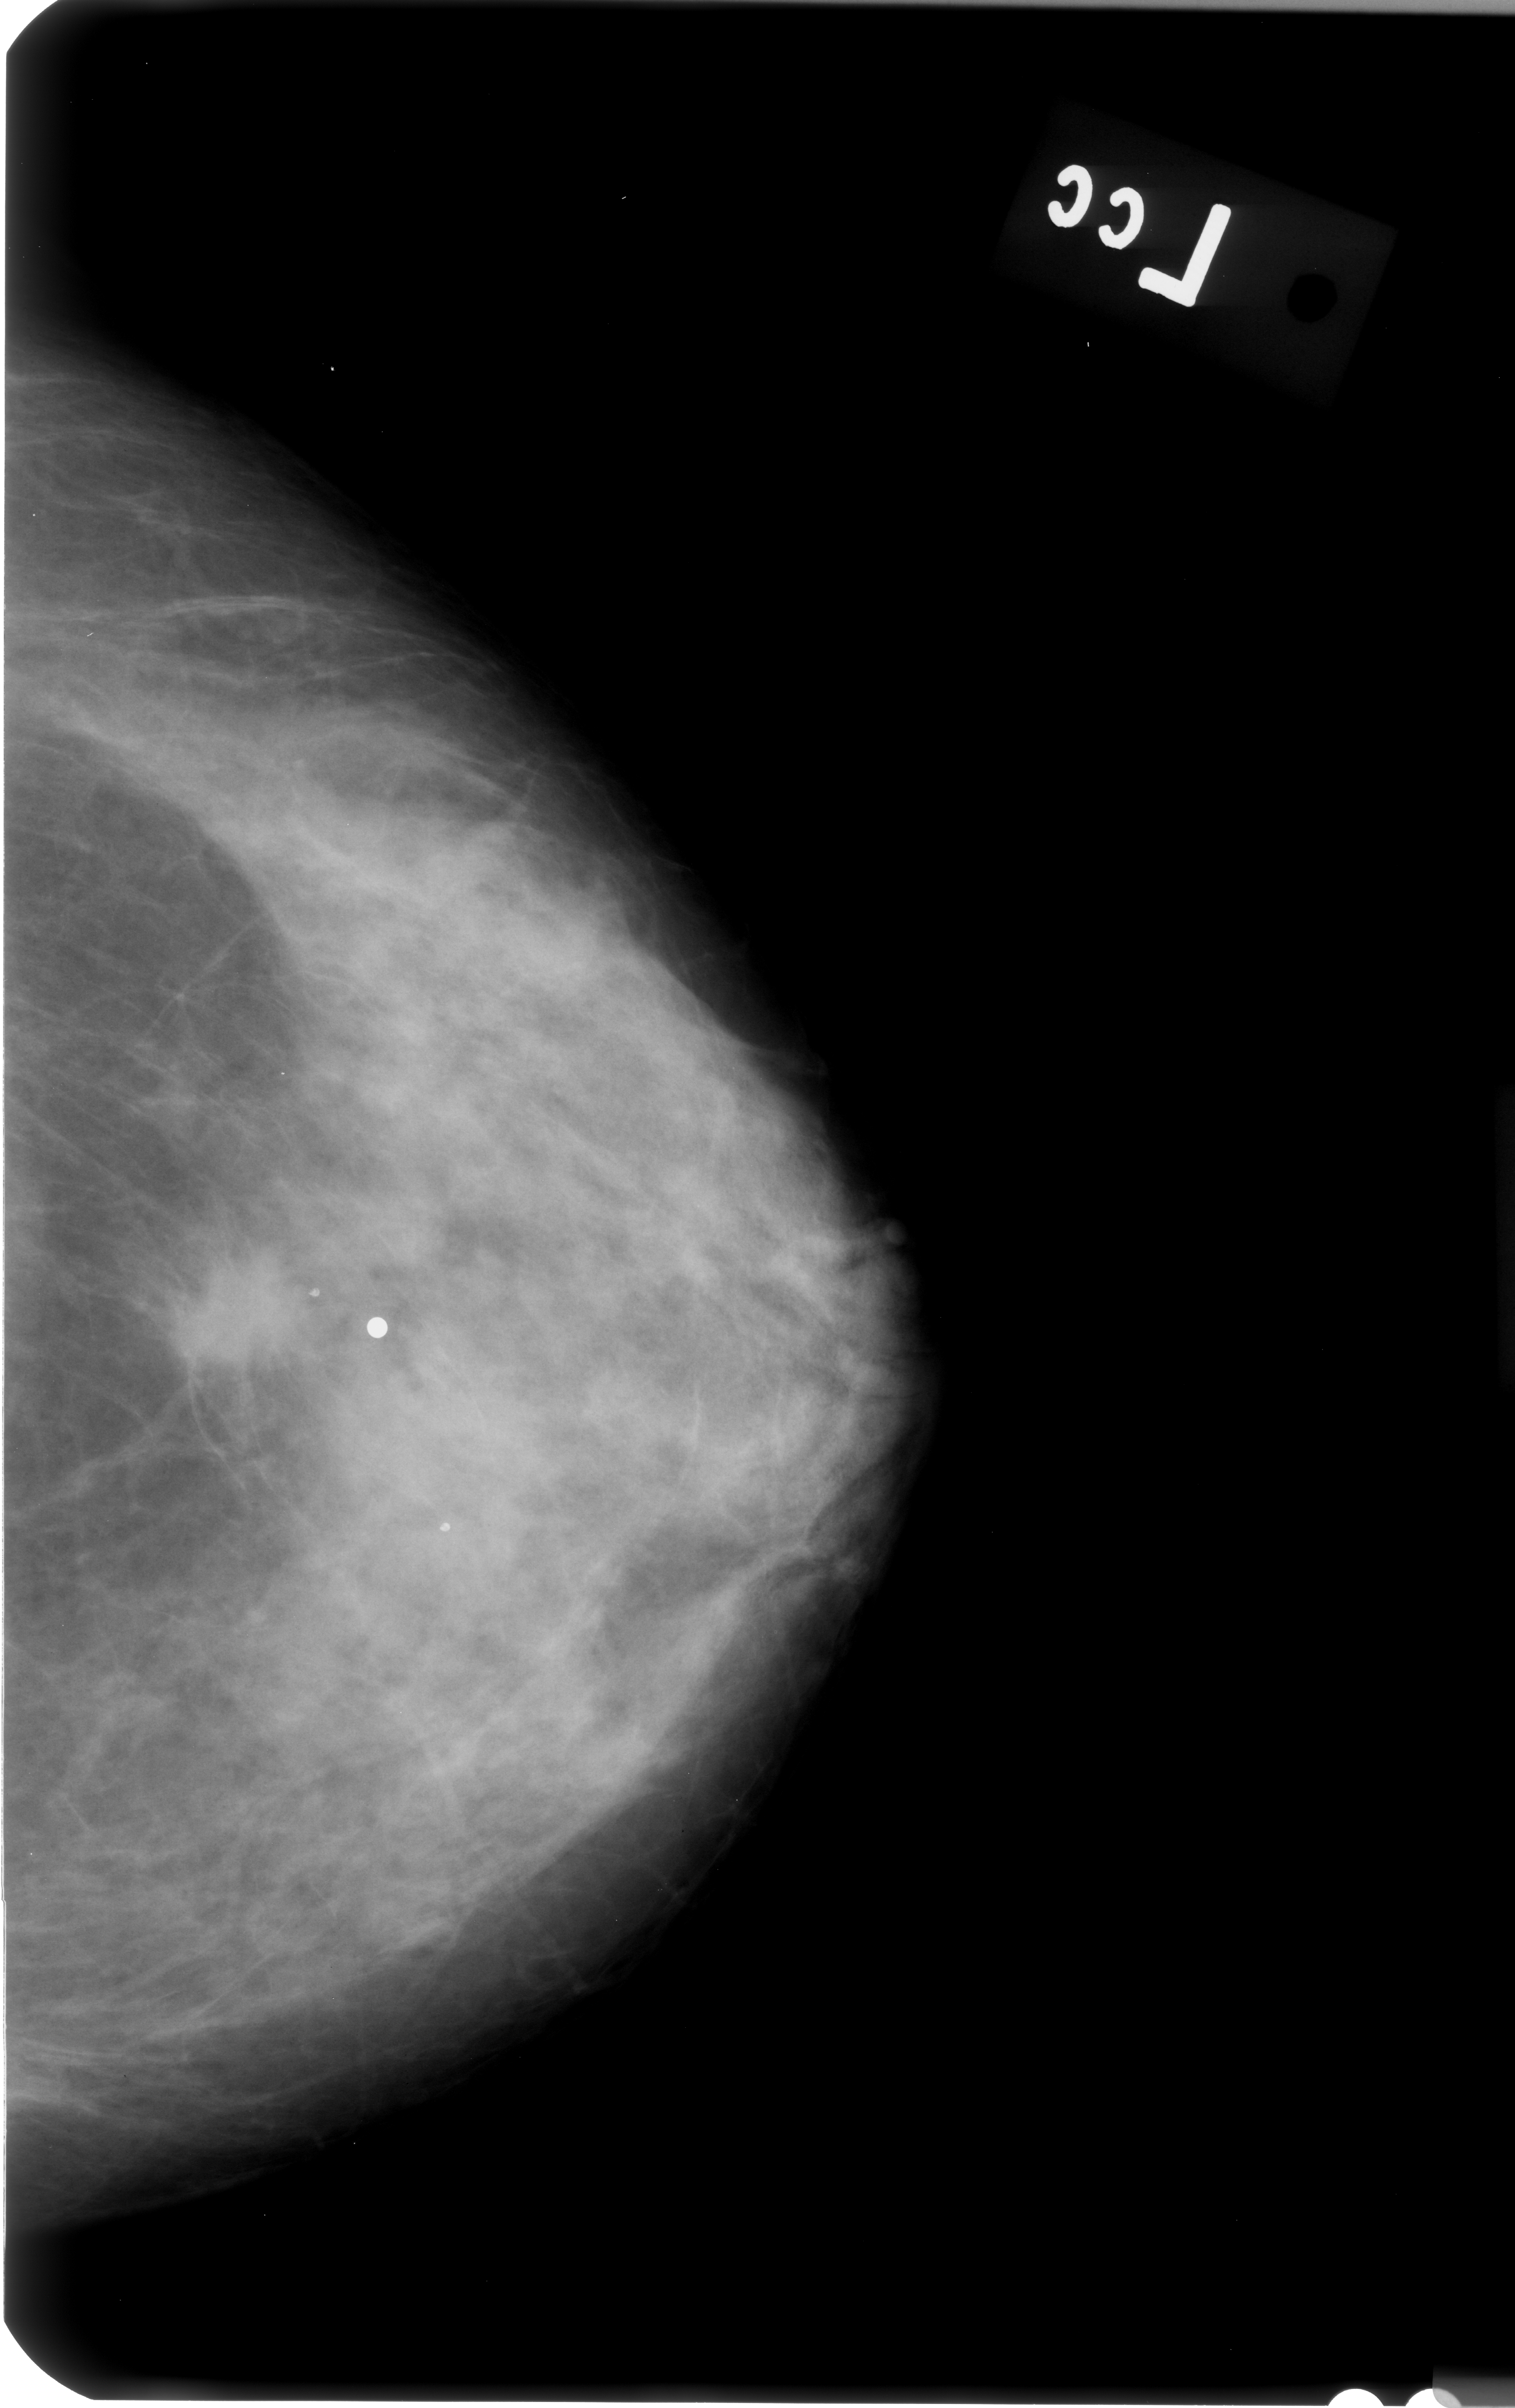
Digitized screen-film mammogram; left breast; craniocaudal (CC) view; breast composition: heterogeneously dense (BI-RADS density category 3 of 4); 1515 × 2408 image matrix.
Expert-marked regions of interest on this film, with their recorded descriptors:
- mass, shape irregular / architectural distortion, margins spiculated; BI-RADS assessment category 4; pathology (as recorded): malignant: bounding box (x1, y1, x2, y2) in pixels: (135, 1213, 332, 1451)